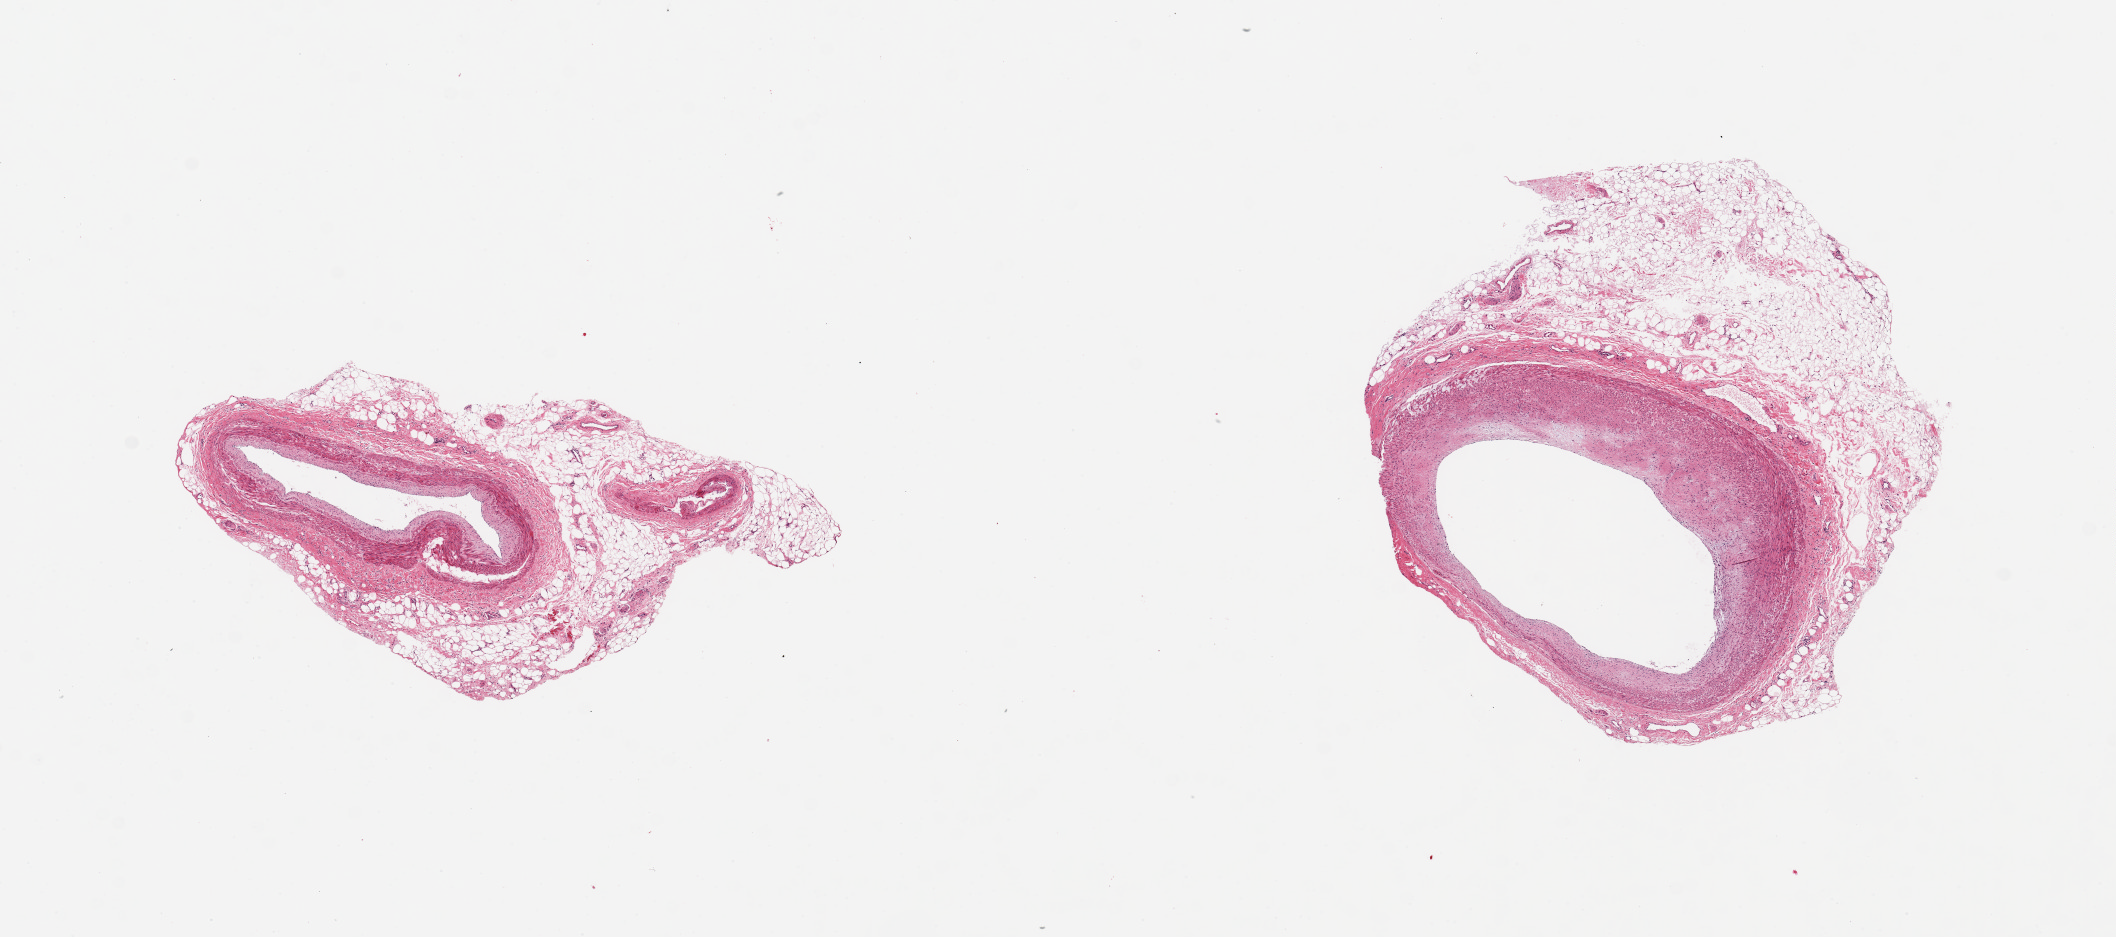
Whole-slide image, haematoxylin and eosin stain, brightfield, shown as a low-resolution overview of the whole scanned area (about 16.7 x 7.4 mm). PAXgene-fixed paraffin-embedded (PFPE) section. Target tissue: coronary artery. Donor tissue sample. Donor: female.
Pathologist's review note for this sample: 2 pieces, 5x3 & 4x4mm; 1 with 20% plaque; both have ~30% adipose, see image.